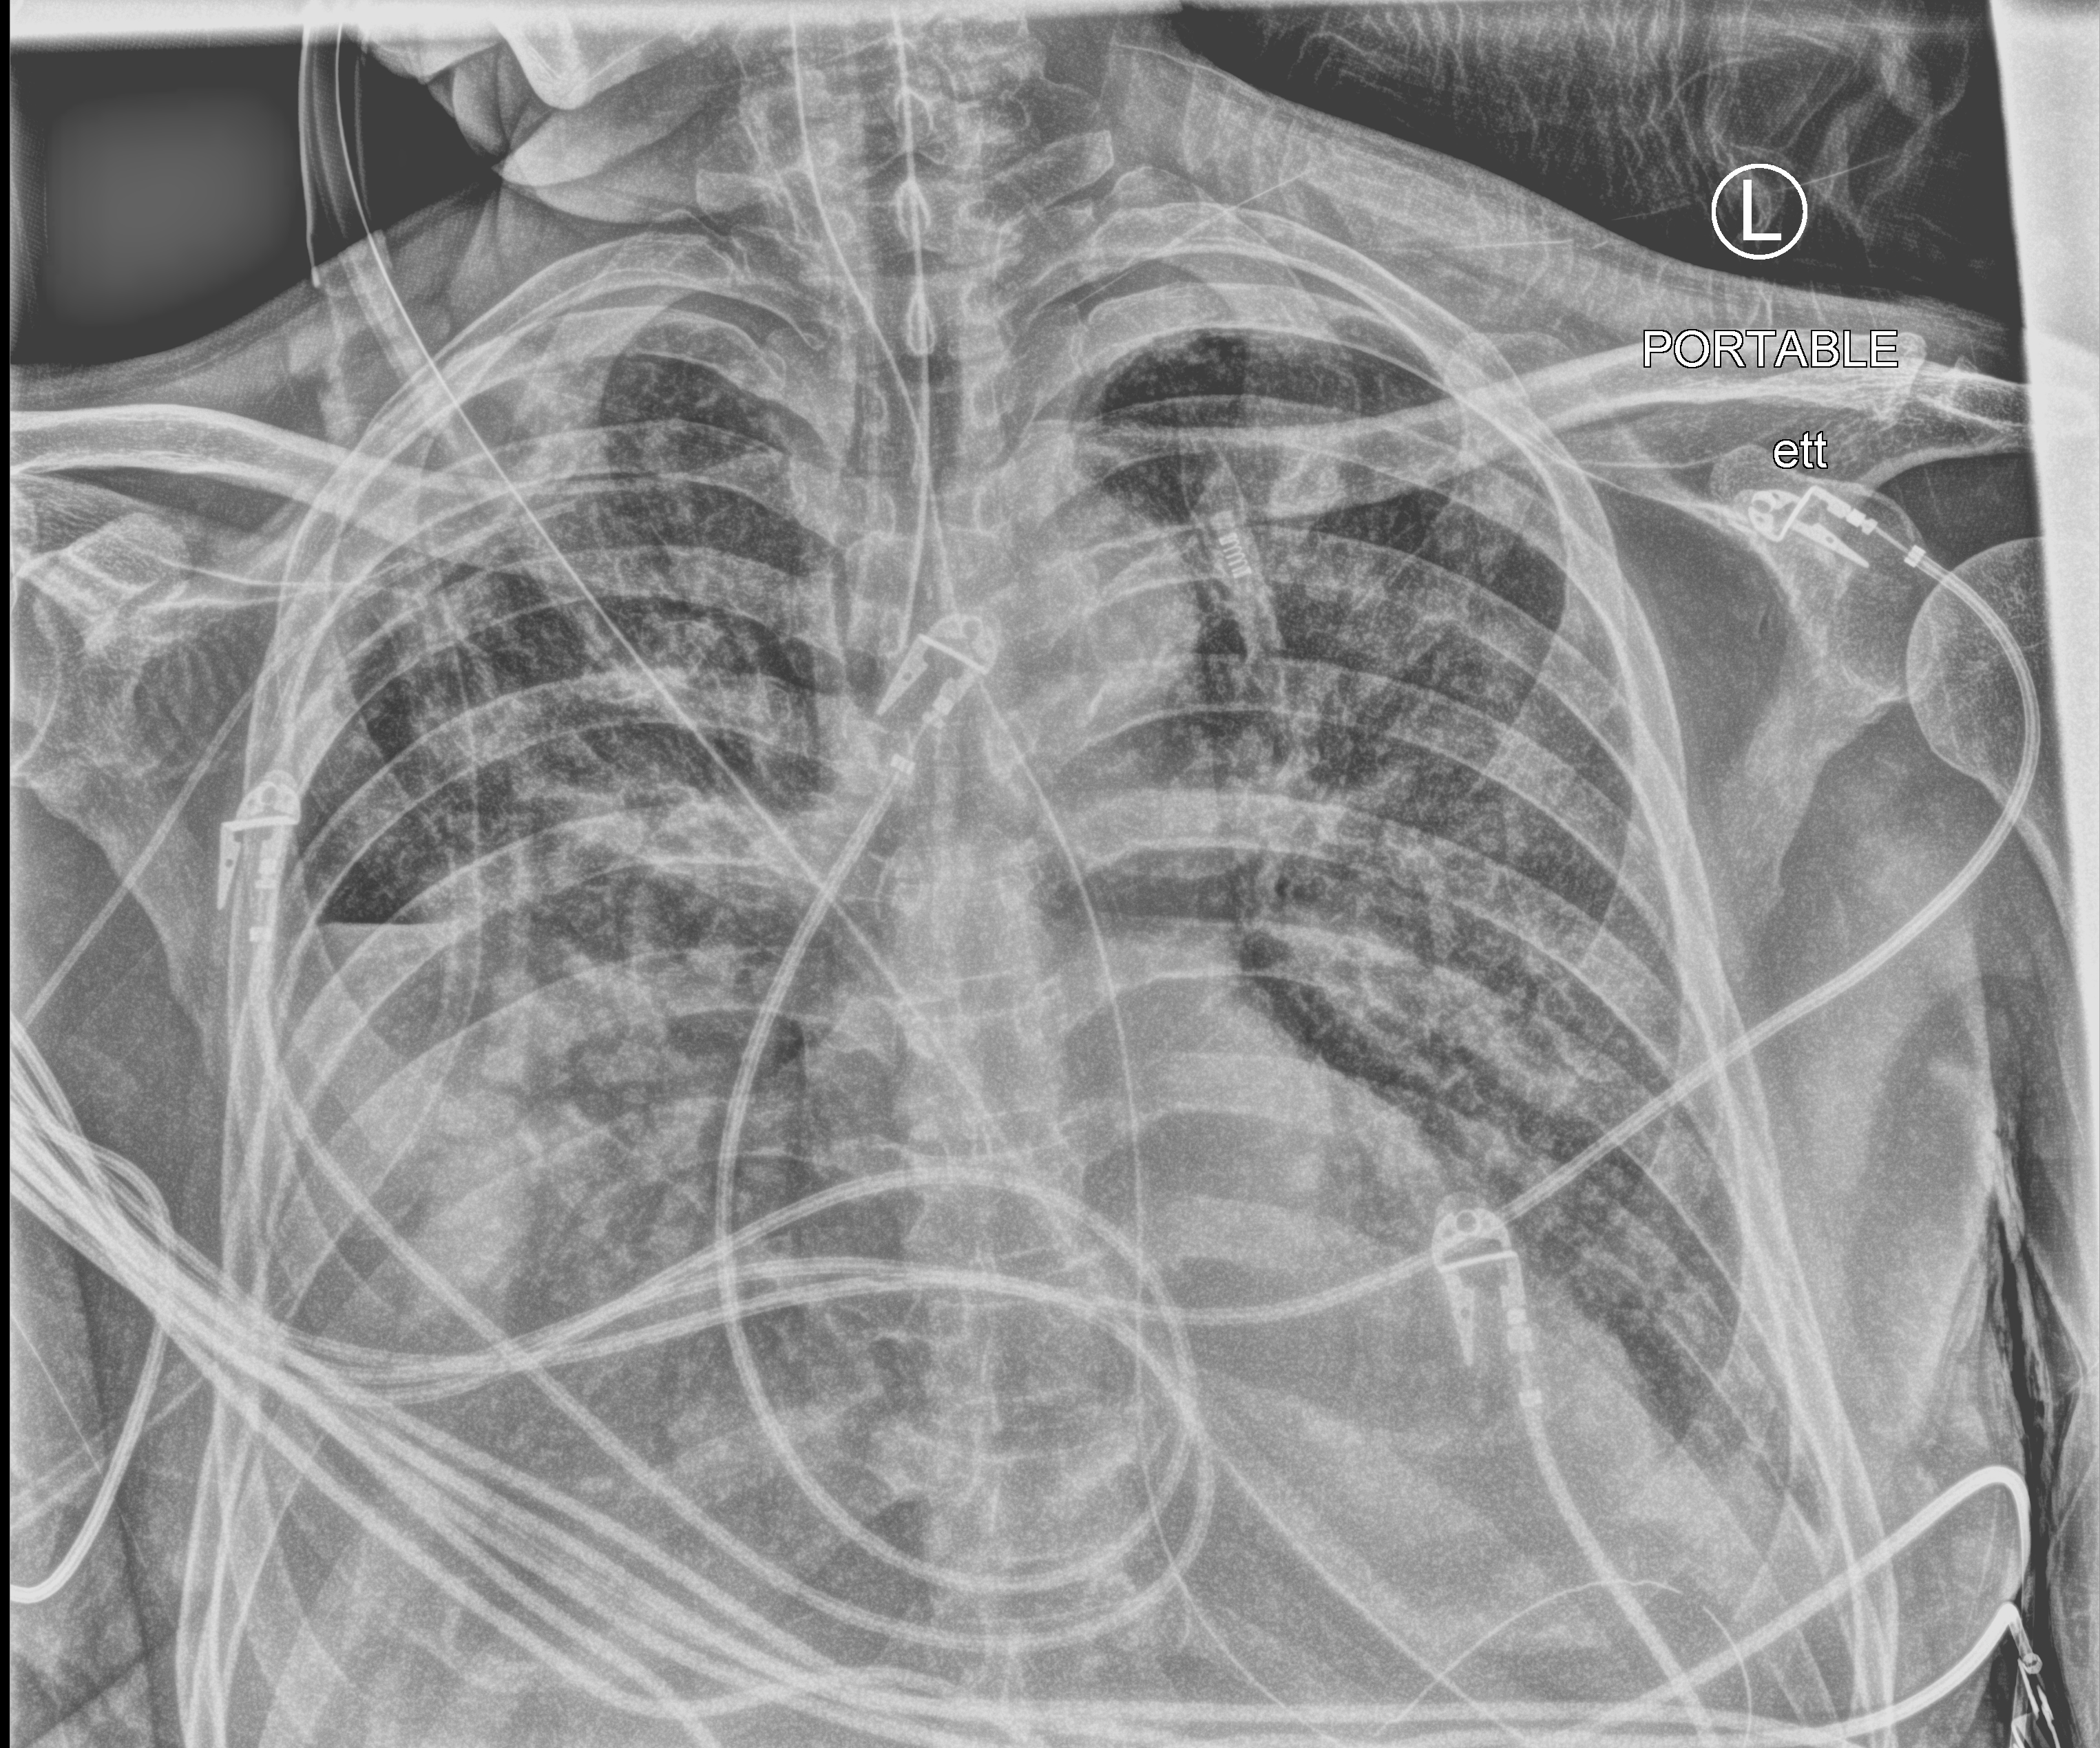
Bedside chest radiograph (computed radiography); anteroposterior (AP) projection. Patient hospitalised with COVID-19; male, aged 60–74 years.
Hospital-stay facts (about this admission, not read from this image; timing relative to this image not recorded): hypertension (admission record): no.